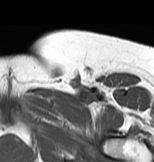
MRI of an extremity soft-tissue mass, one axial slice; position 55 of 83 along the scan axis; MR volume resampled by the dataset authors to the PET/CT grid (not the native acquisition matrix); 3.27 mm slice thickness; 154 × 162 image matrix, field of view 150 × 158 mm. Female patient. From the clinical record (not read from this slice): histological type: myxofibrosarcoma; grade: intermediate; site of the primary tumour: left thigh.
Annotated regions visible in this slice (expert contour drawn on MRI and transferred to this co-registered scan by the dataset authors):
- gross tumour volume including surrounding oedema: box from (x=35, y=87) to (x=116, y=115) px